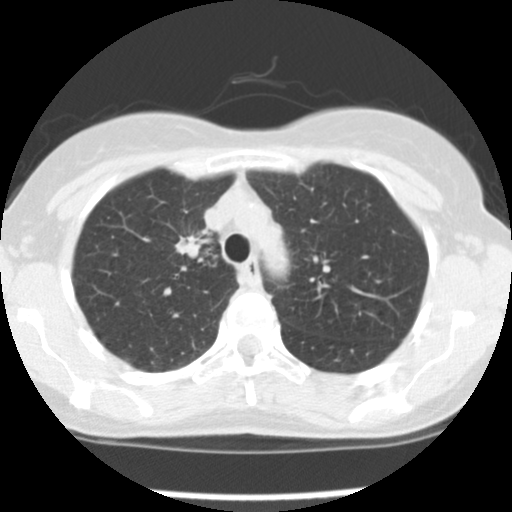
Axial slice from a low-dose chest CT screening exam. First (baseline) screen. Lung window (W 1500 / L -600 HU). 2.5 mm slice thickness. 120 kVp. Slice 118 of 157 in the series. Female participant, aged 57 years at enrolment. Current smoker at enrolment.
Expert-annotated lung lesion, bounding box [x1, y1, x2, y2] px = [165, 227, 217, 273]. Screening reader's record for this exam (one nodule recorded; not confirmed to be the boxed lesion): non-calcified nodule or mass ≥4 mm, left upper lobe, 7 × 6 mm, poorly defined margins, ground glass attenuation. Note: the box lies in the patient's right hemithorax on this image, whereas the reader's record names the left lung; they may be different findings. Participant outcome: lung cancer diagnosed 15 days after this screen — adenocarcinoma, NOS, right upper lobe, moderately differentiated (G2), stage IA (AJCC 6th edition), 15 mm at pathology.